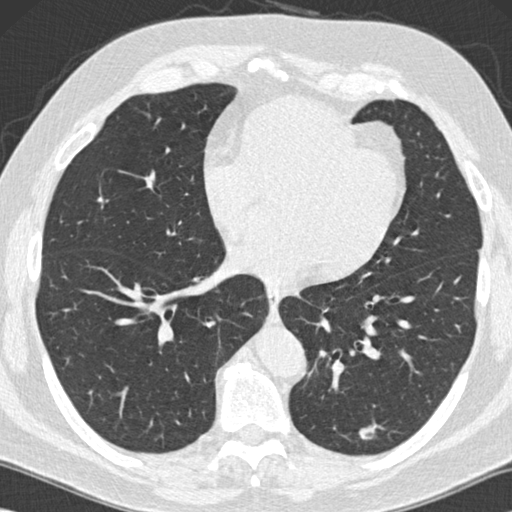
Low-dose screening chest CT, one axial slice; slice 56 of 152 in the series (ordered by position); reconstruction kernel B30f; 120 kVp; lung window (W 1500 / L -600 HU); 512 × 512 image matrix.
Annotated regions visible in this slice (outlined manually by an expert reader):
- lesion 1 (tumor, lower lobe of left lung): bounding box (x1, y1, x2, y2) in pixels: (359, 426, 375, 440)